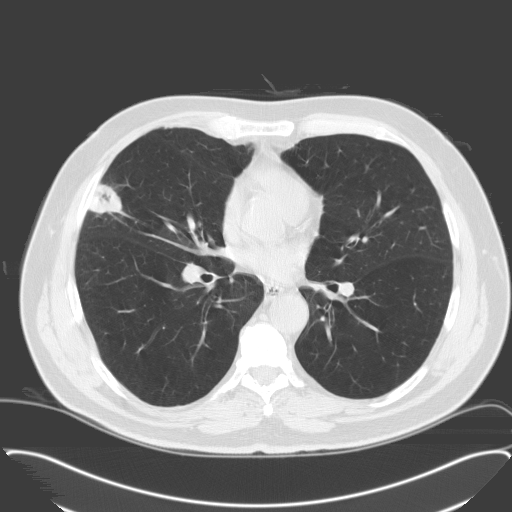
Axial slice from a low-dose chest CT screening exam; third screening round (two years after baseline); lung window (W 1500 / L -600 HU); 512 × 512 image matrix, field of view 400 × 400 mm. Male participant, aged 65 years at enrolment. Former smoker at enrolment.
Lesion marked by an expert reader, box from (x=72, y=180) to (x=129, y=234) px. Reader record for this screening exam (exam-level; its link to the box is not recorded): non-calcified nodule or mass ≥4 mm, right middle lobe, 28 × 23 mm, spiculated (stellate) margins, soft tissue attenuation, pre-existing on the prior screen: no.